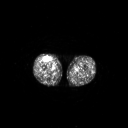
FDG PET of an extremity soft-tissue mass (from a PET/CT study), one axial slice. Slice 251 of 311 in the series (ordered by position). 128 × 128 image matrix. Patient: male, 56 years. From the clinical record (not read from this slice): histological type: pleiomorphic leiomyosarcoma; grade: intermediate; site of the primary tumour: right thigh.
Structures marked on this image (expert contour drawn on MRI and transferred to this co-registered scan by the dataset authors):
- gross tumour volume including surrounding oedema: box from (x=43, y=56) to (x=51, y=62) px